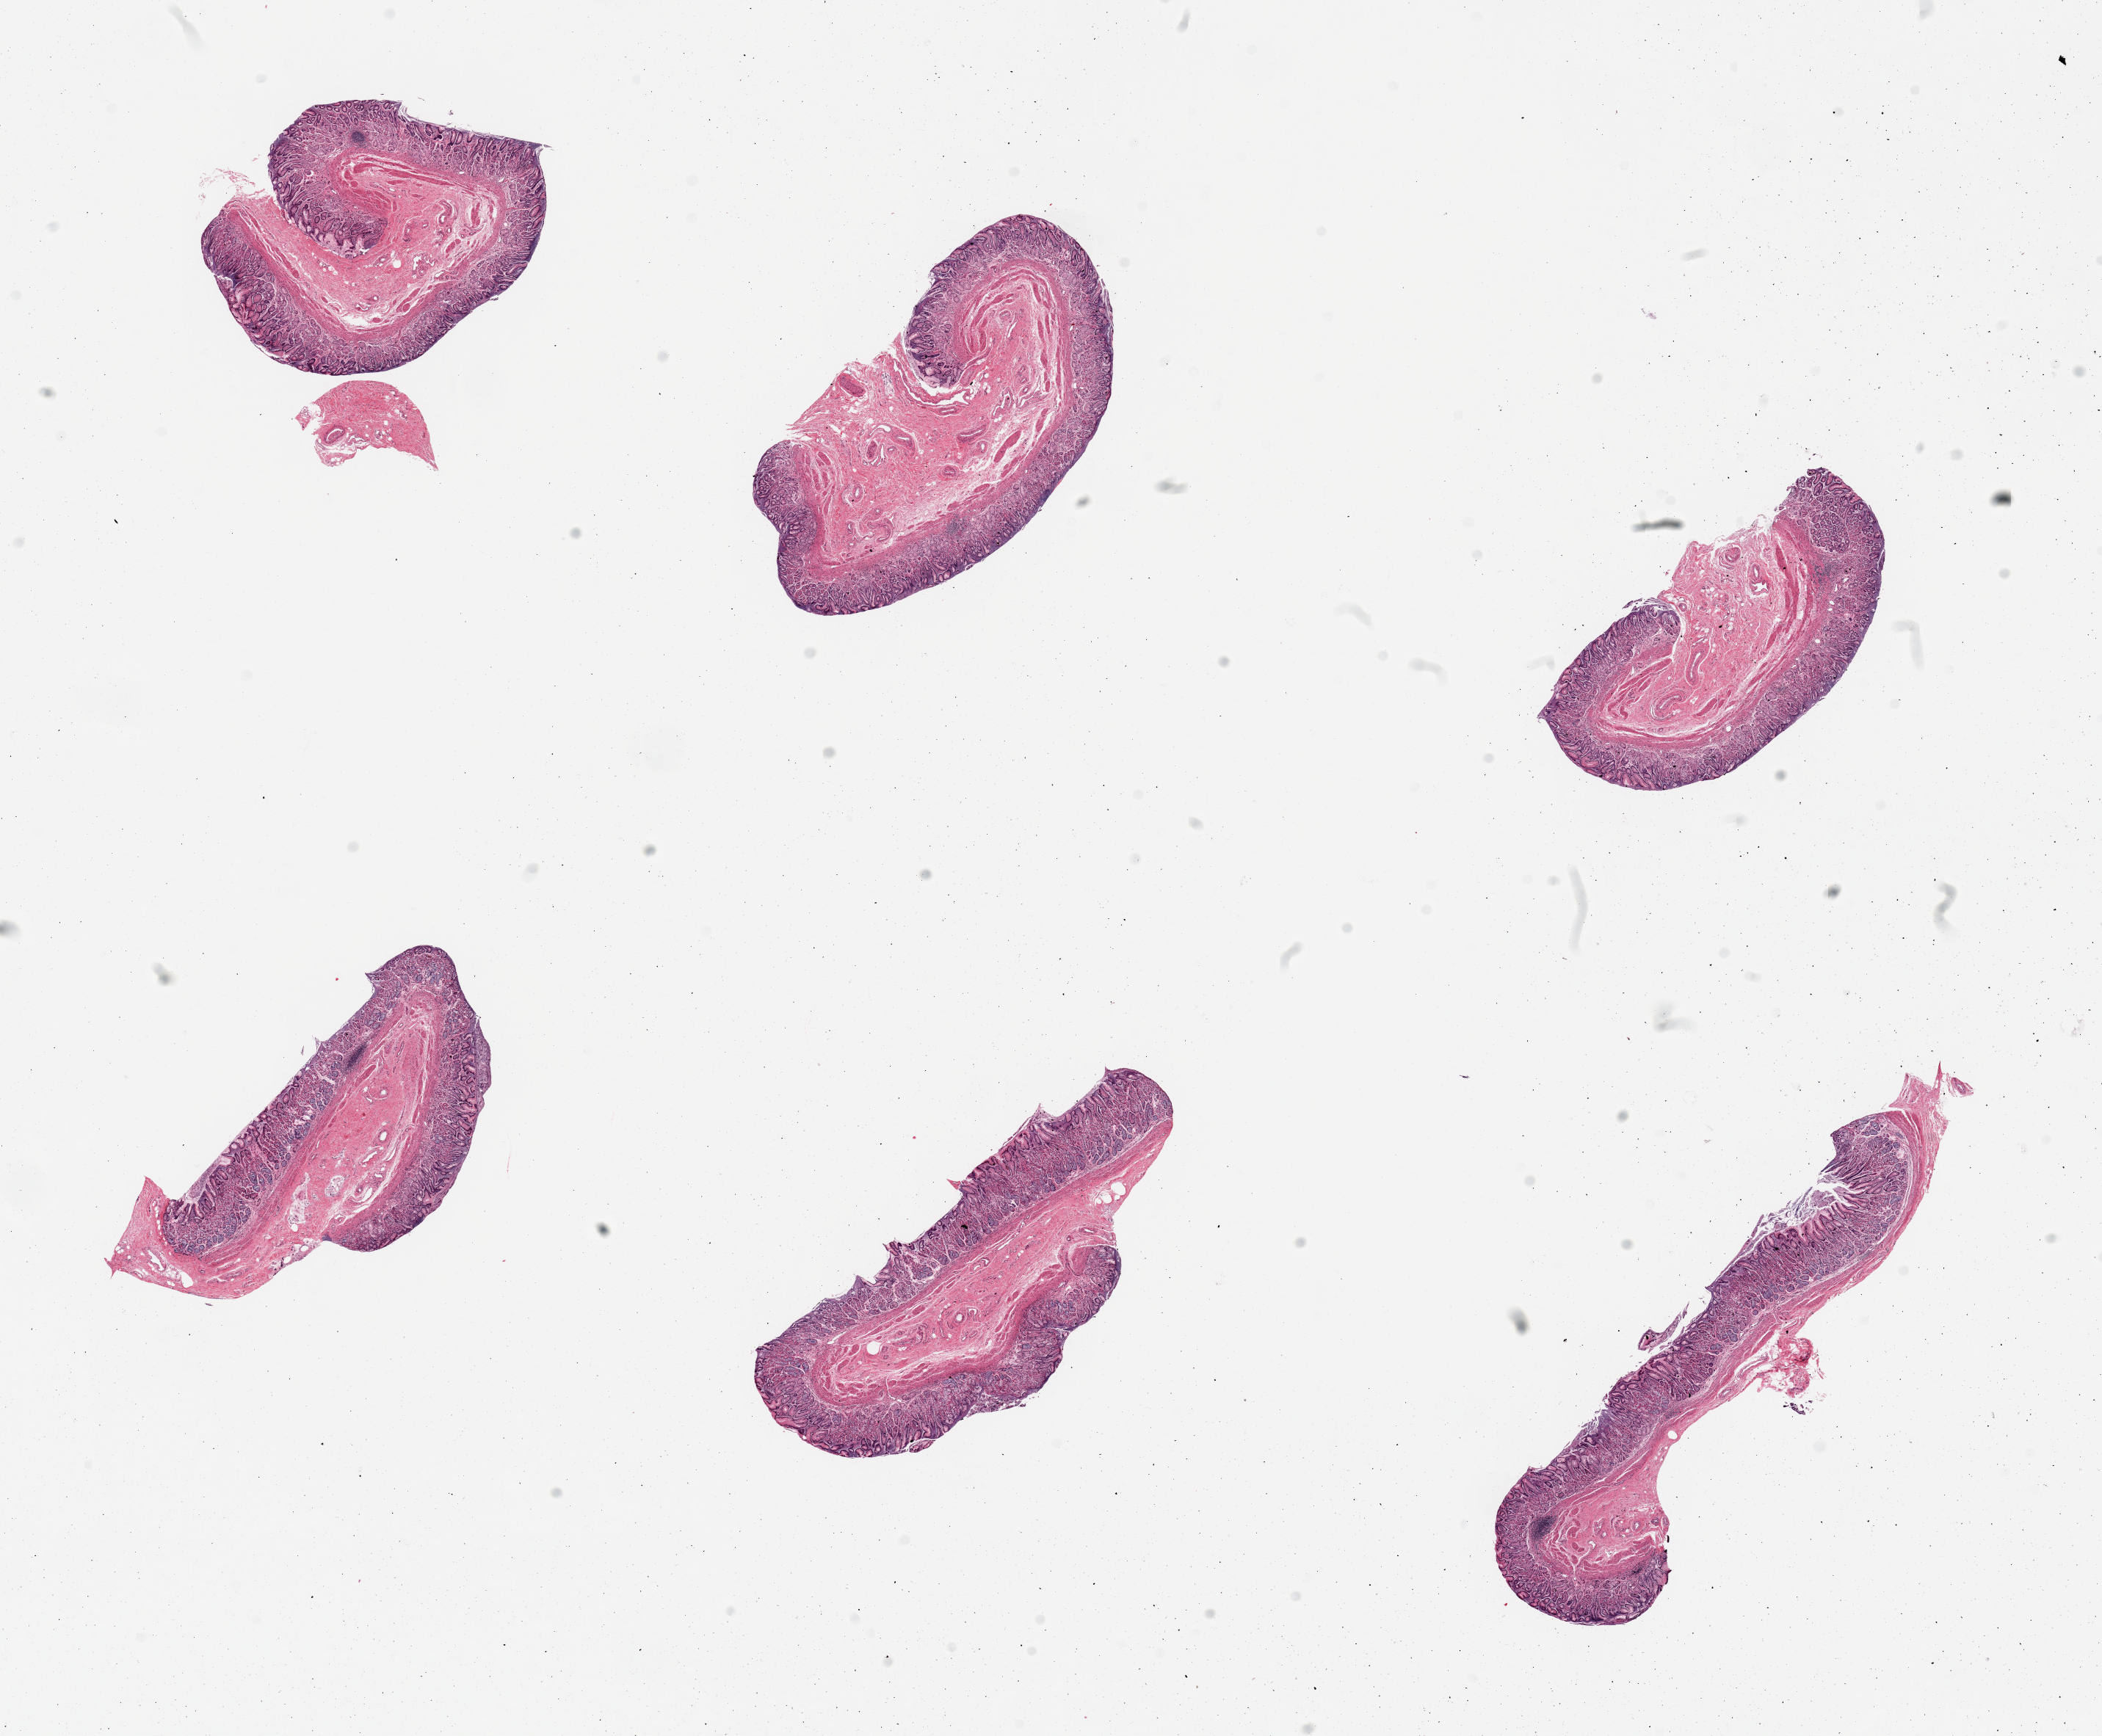
H&E whole-slide image — low-resolution overview of the scanned area, about 22.6 x 18.7 mm, PAXgene-fixed, paraffin-embedded tissue, target tissue: stomach, donor tissue sample. Donor sex: female.
Reviewer comment on this tissue sample: 6 pieces, mucosa up to ~0.6mm, 20-50% thickness.